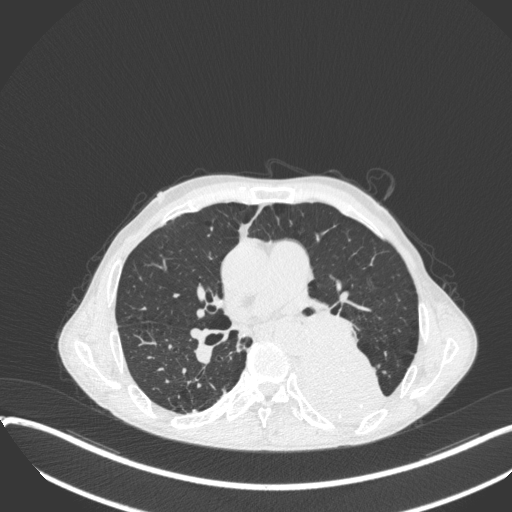
Chest CT, one axial slice; position 203 of 400 along the scan axis; reconstruction kernel B31f; lung window (W 1500 / L -600 HU); 1 mm slice thickness; 512 × 512 image matrix. Male patient, age 57 years. From the clinical record (not read from this slice): clinical TNM (as recorded): T4 N0 M0.
Outlined on this slice (rectangle marked by the reading radiologist):
- lung tumour (recorded histology: squamous cell carcinoma): bounding box (x1, y1, x2, y2) in pixels: (298, 336, 391, 427)